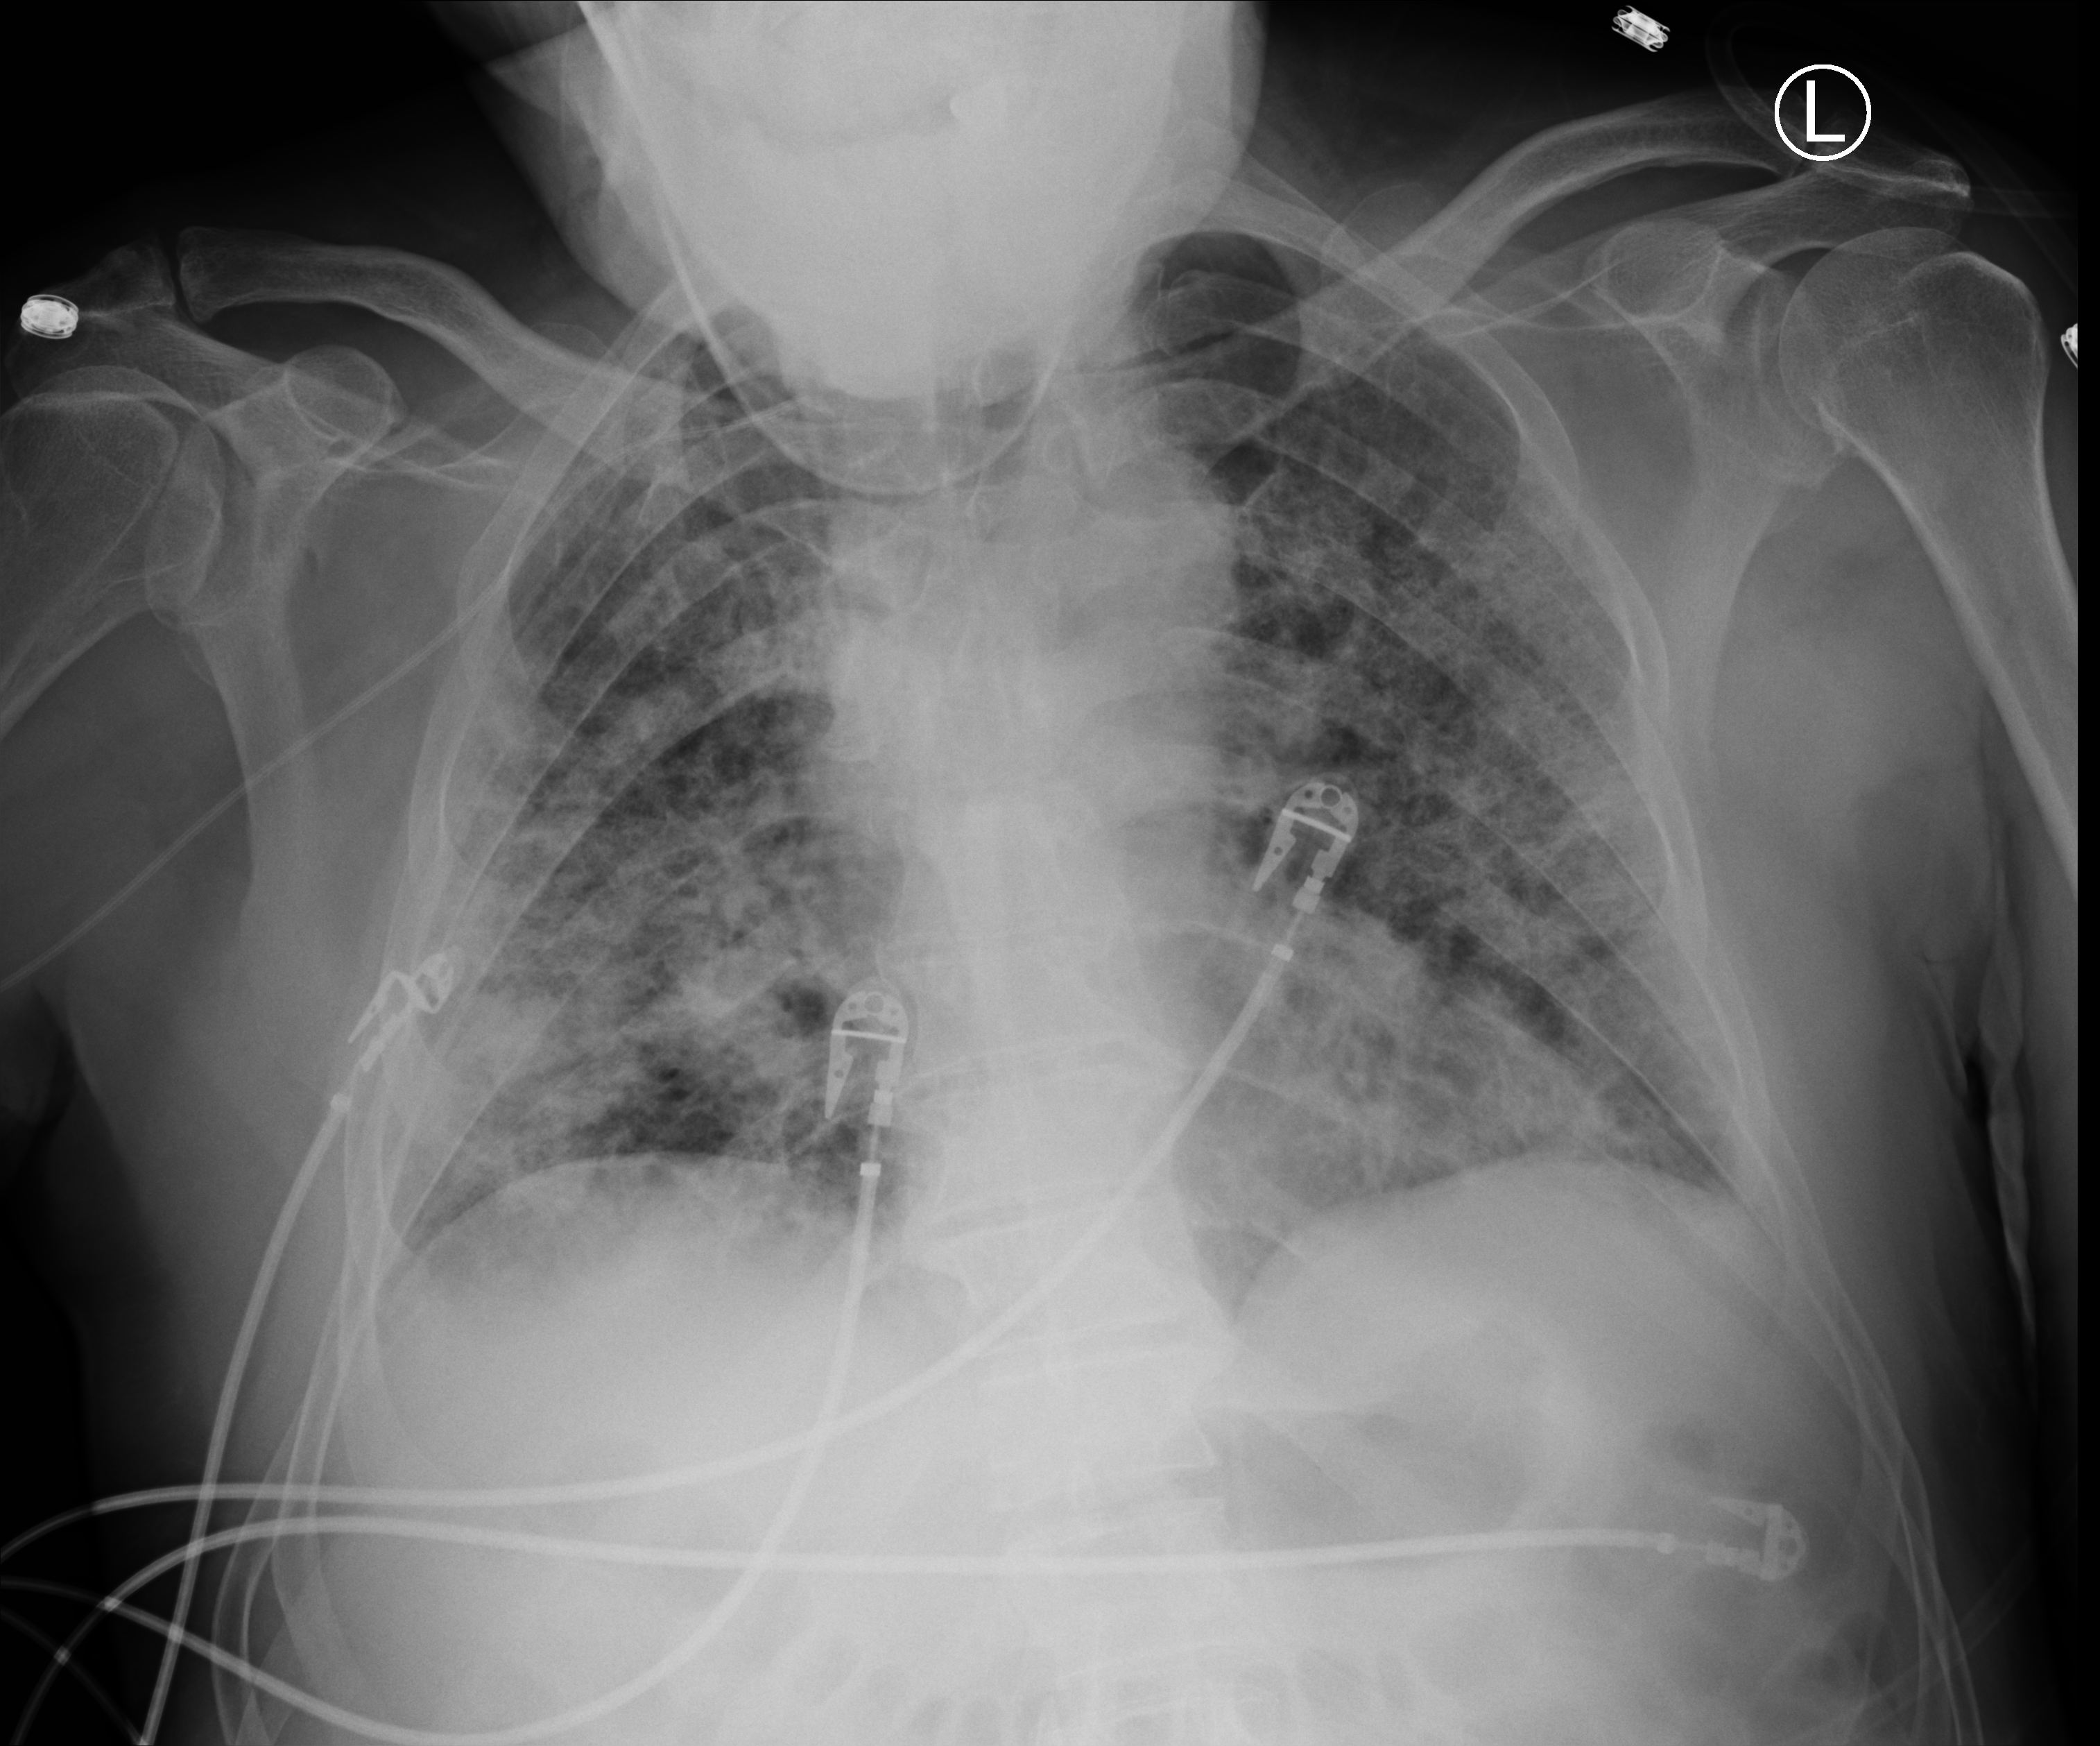
Chest X-ray (portable), anteroposterior (AP) projection. Male patient hospitalised with COVID-19, age 60–74 years.
Admission-level facts for this patient (not findings on this image; timing relative to this image not recorded): admitted to intensive care during this hospital stay: yes; smoking status (admission record): never.